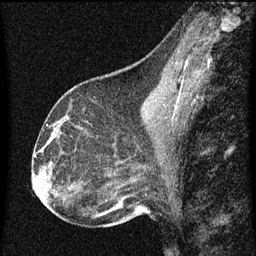
Breast MRI (dynamic contrast-enhanced), one sagittal slice; slice 31 of 60 in the series (ordered by position); dynamic contrast-enhanced series, image 2 of 3 at this slice position (ordered by acquisition); 1.5 T; TE 4.2 ms, TR 8 ms; 2 mm slice thickness; 256 × 256 image matrix. Female patient, age 43 years.
Annotated regions visible in this slice (semi-automatically segmented with operator editing):
- analysis volume of interest (the breast-tissue region the enhancement analysis was run in; not a lesion): bounding box [x1, y1, x2, y2] px = [53, 104, 100, 151]
- tumour enhancement mask (voxels above the 70 % enhancement threshold inside the analysis volume of interest): [59, 120, 67, 123]